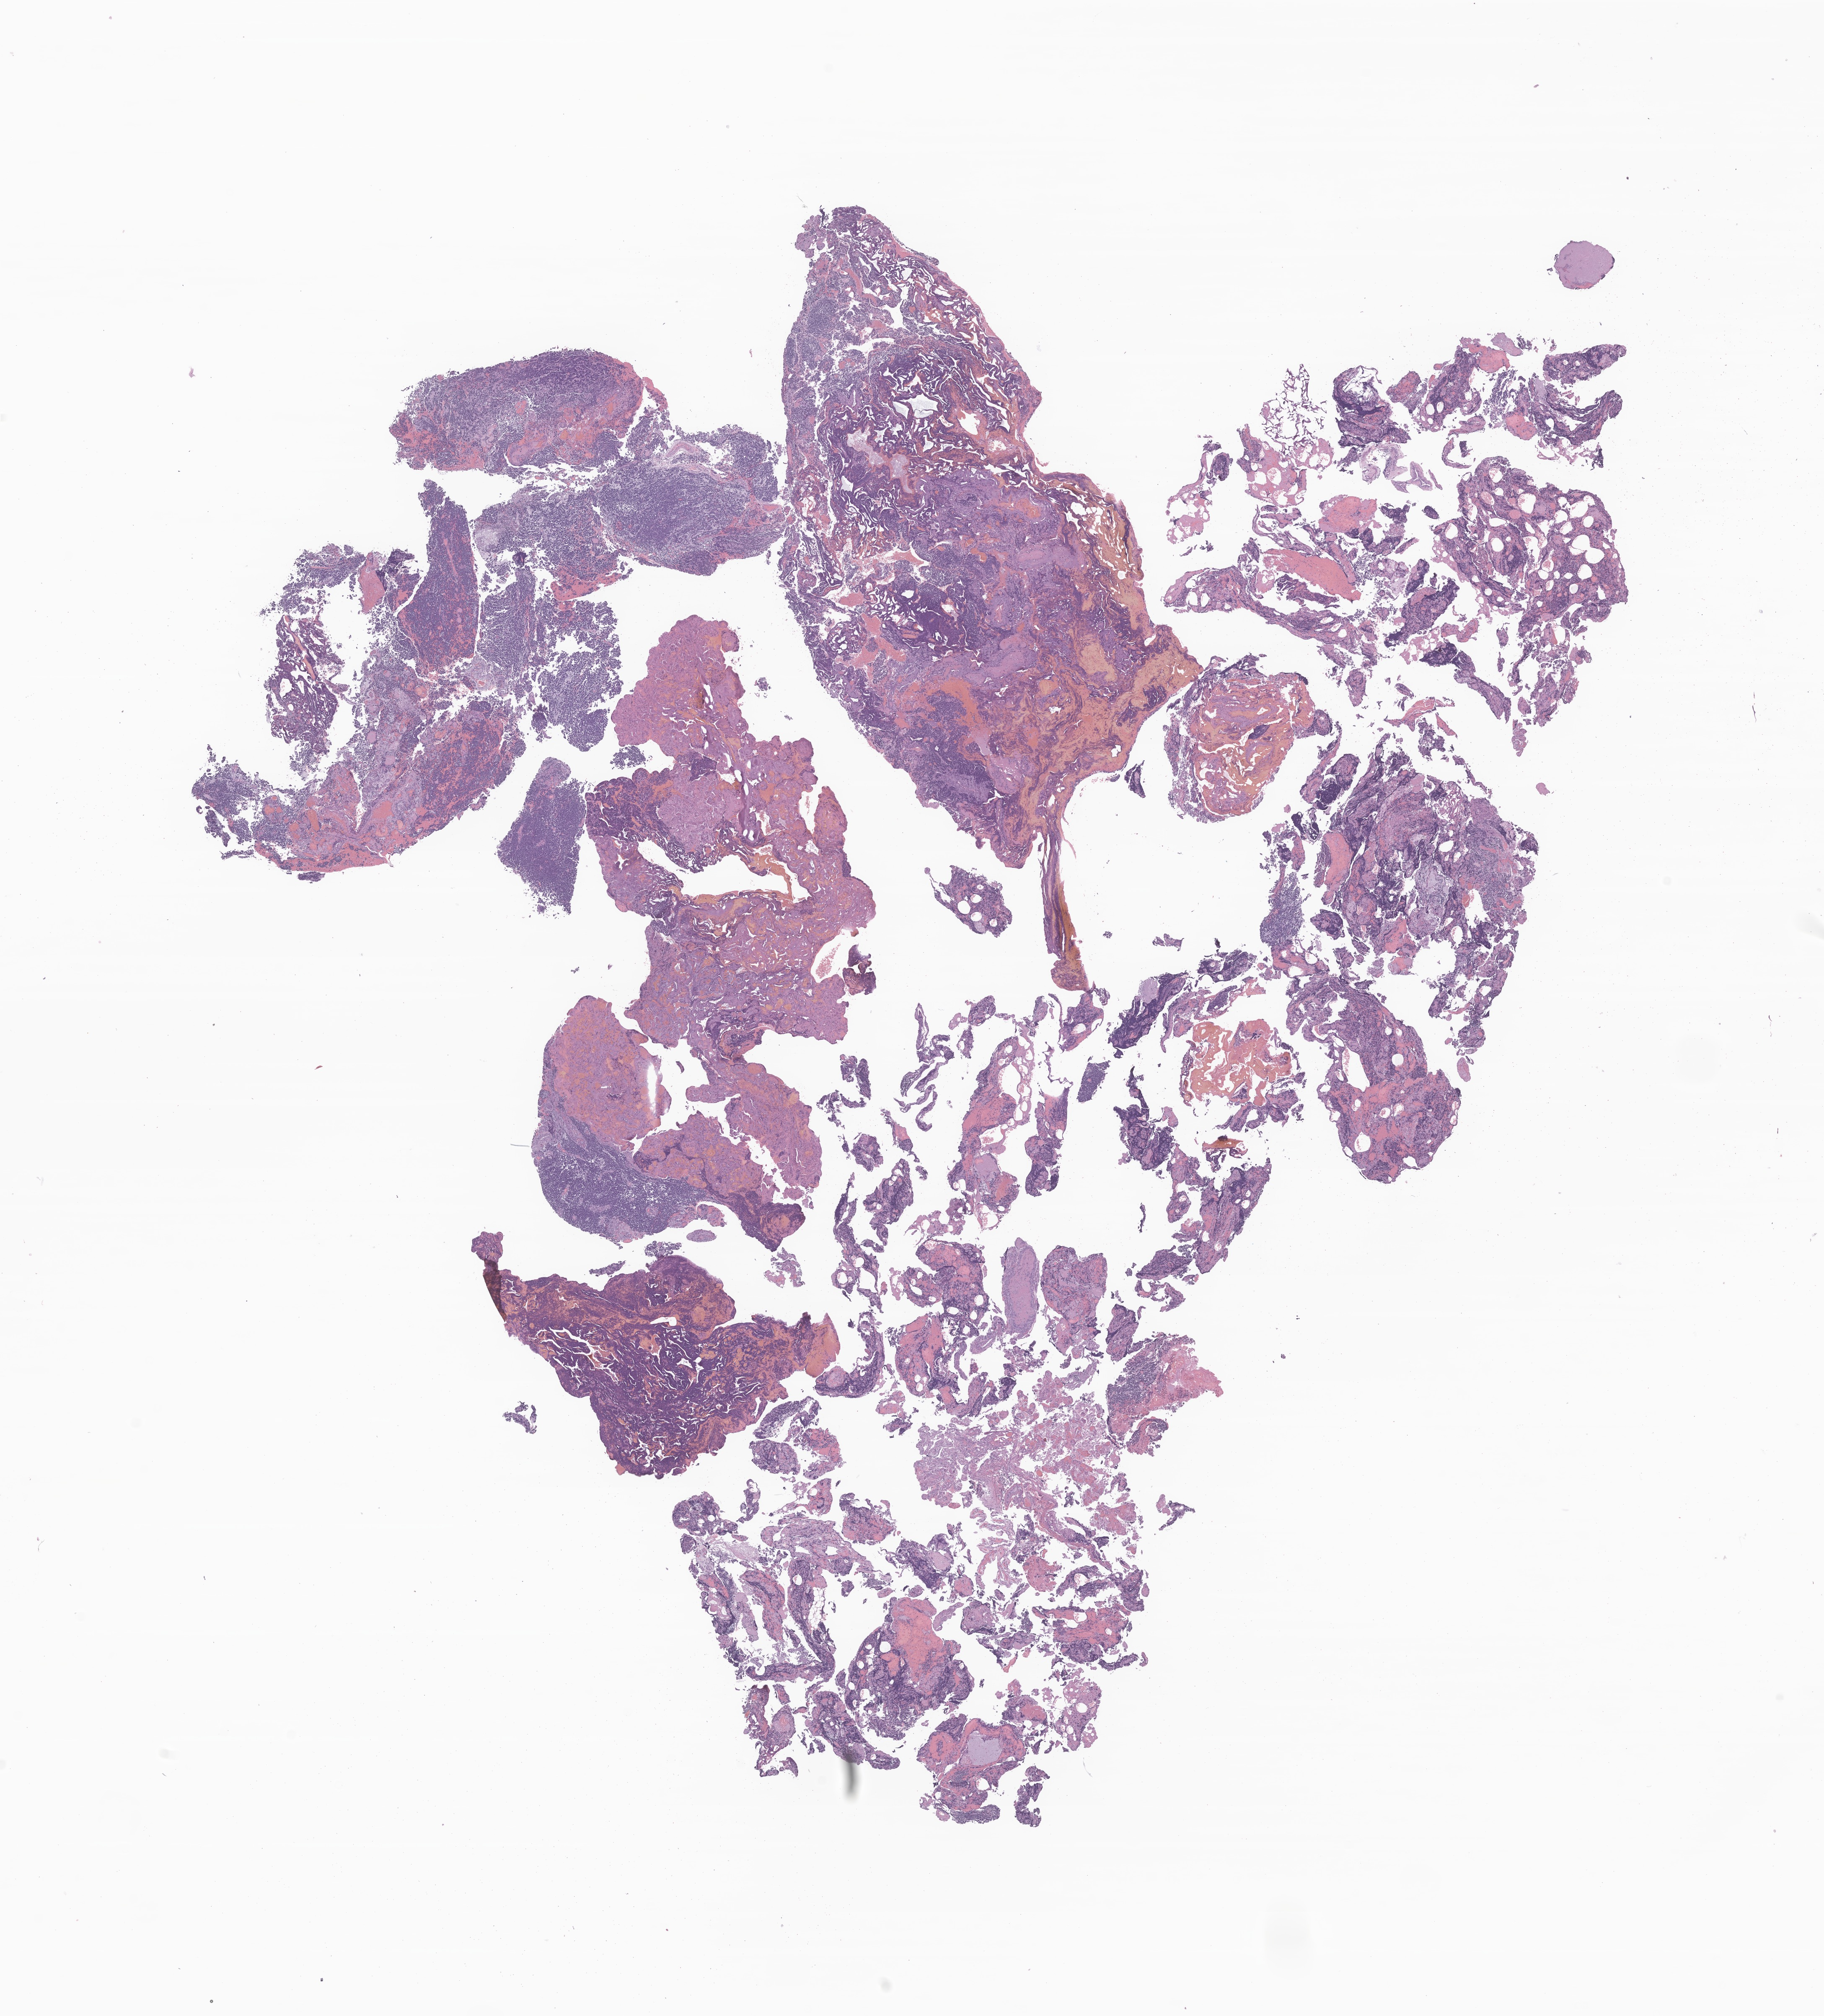
H&E whole-slide image of tumor tissue from the brain — a low-resolution overview of the entire scanned area, about 18.4 x 20.3 mm; formalin-fixed paraffin-embedded section. Patient female; age 163 months (13 years 7 months).
• recorded diagnosis: Medulloblastoma, NOS